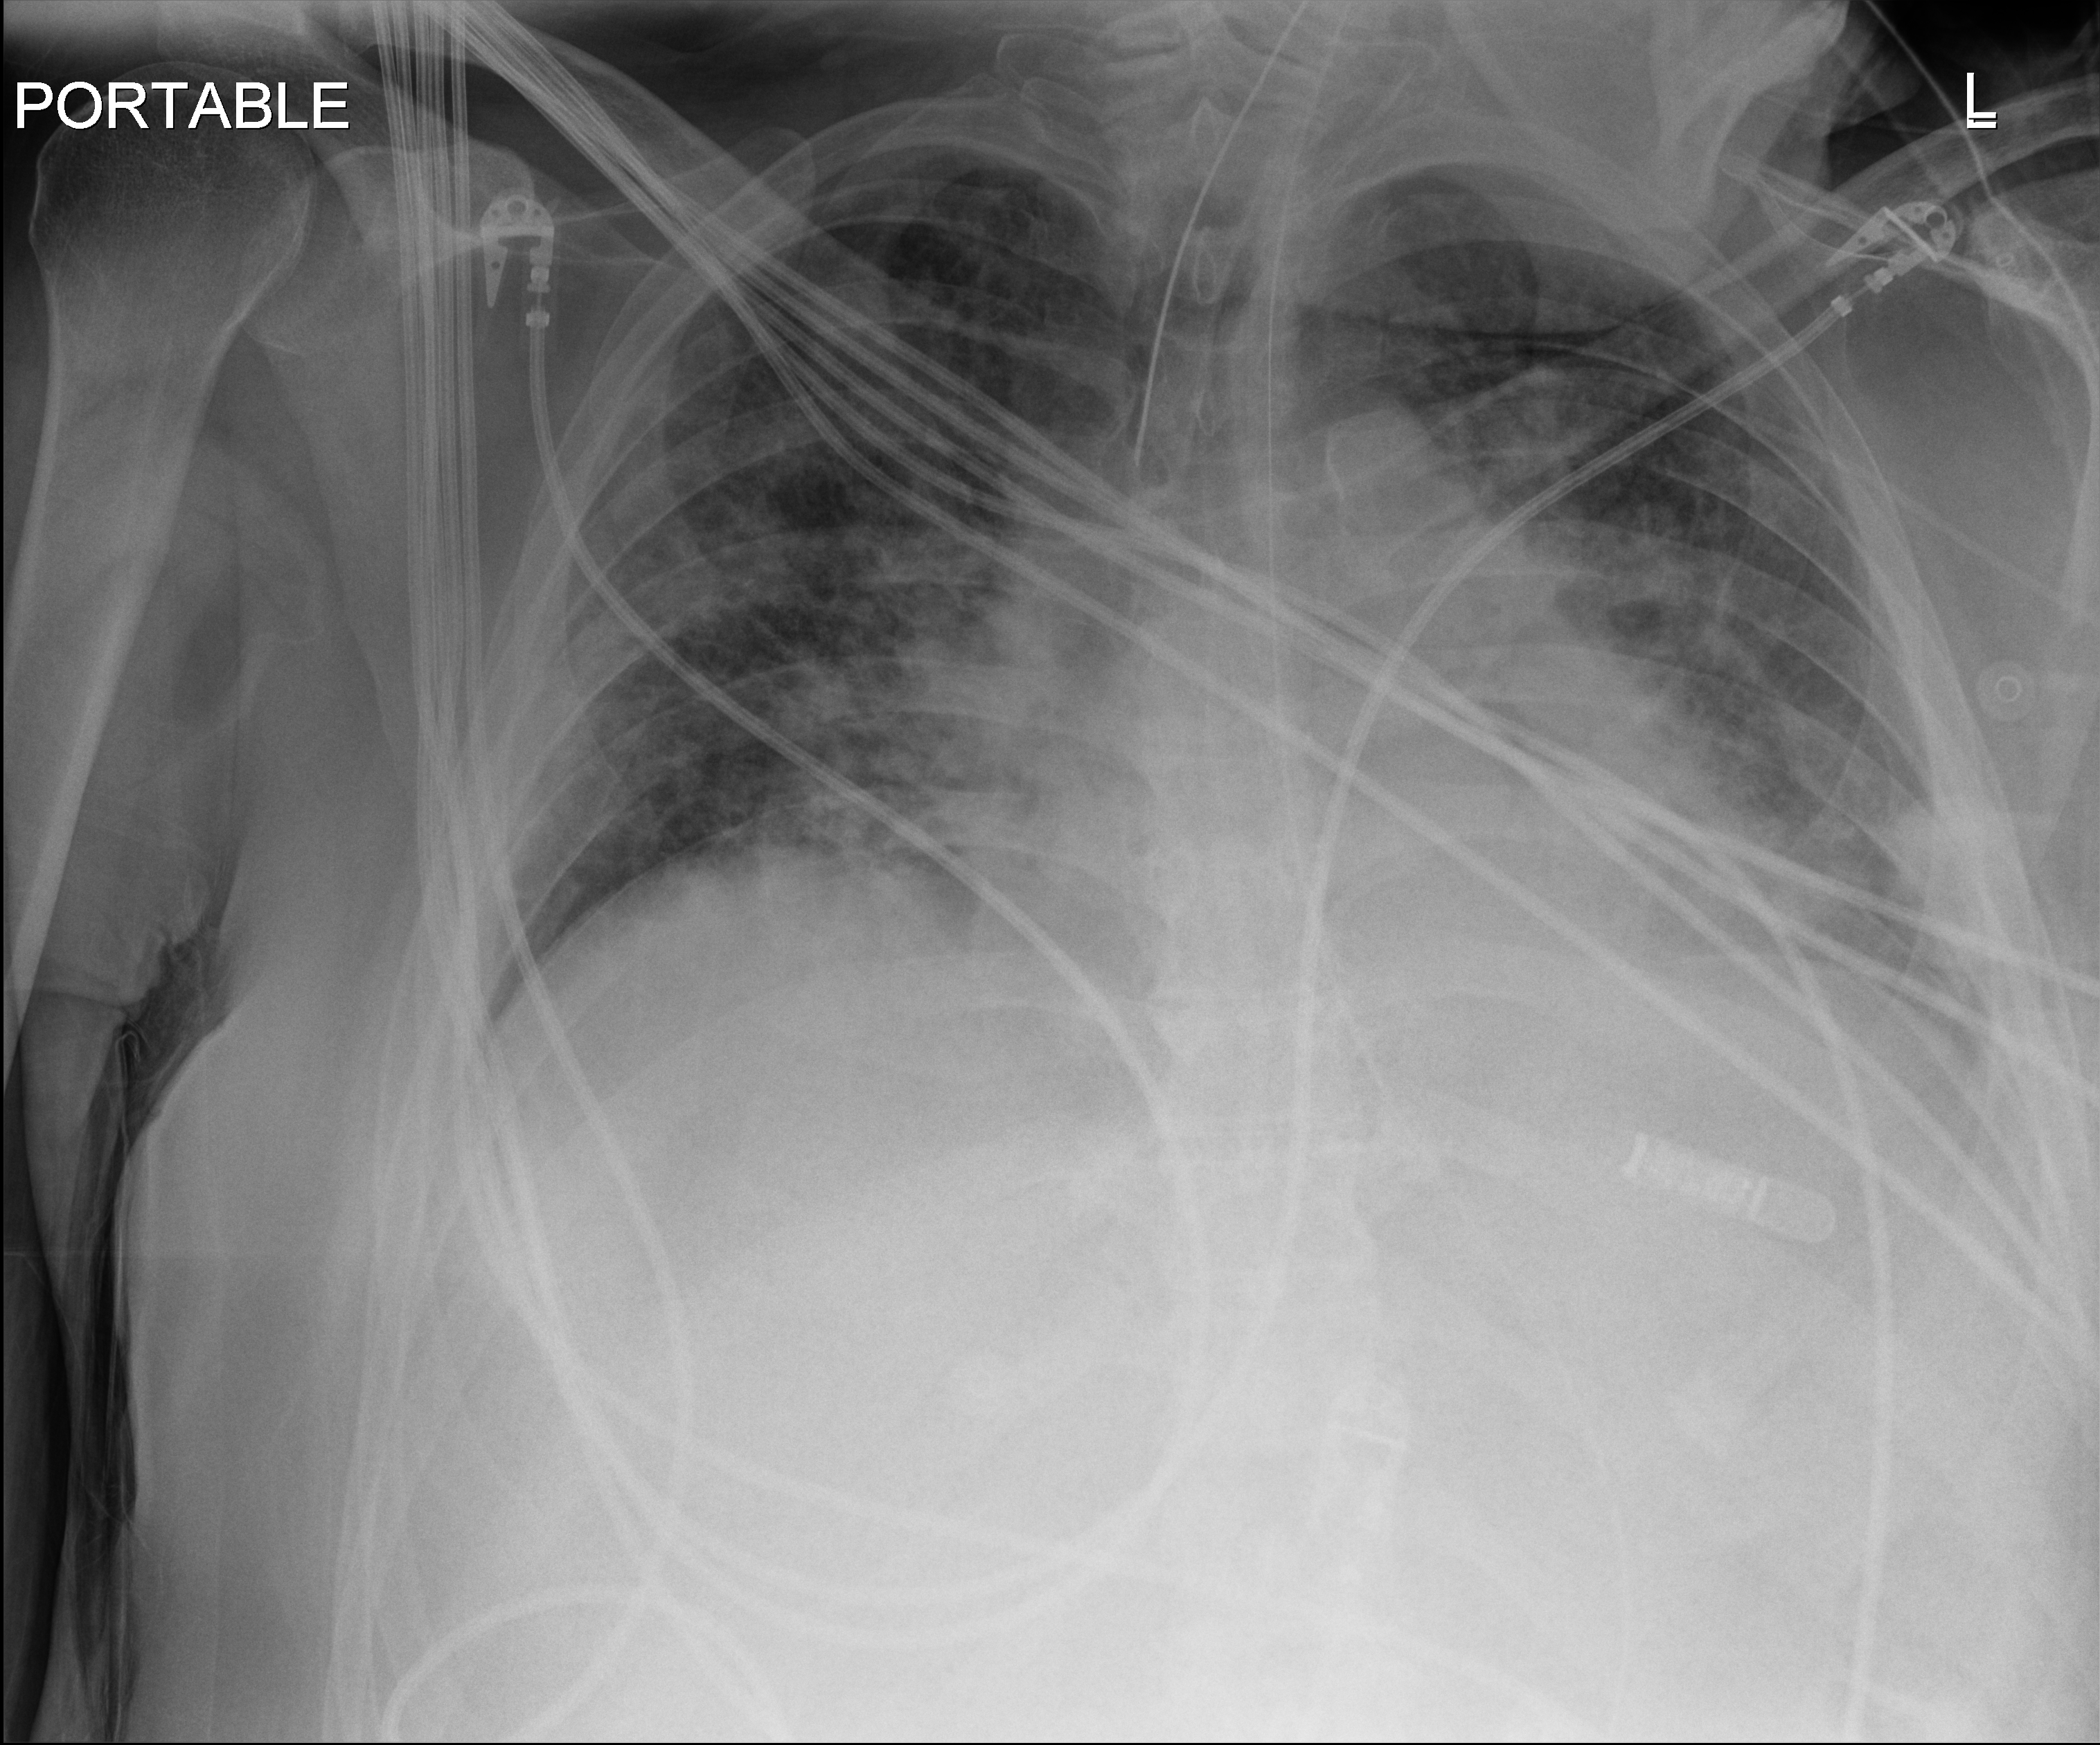
Bedside chest radiograph (digital radiography), anteroposterior (AP) projection. Patient hospitalised with COVID-19; male, aged 18–59 years.
Admission-level facts for this patient (not findings on this image; timing relative to this image not recorded):
- length of hospital stay: 39 days